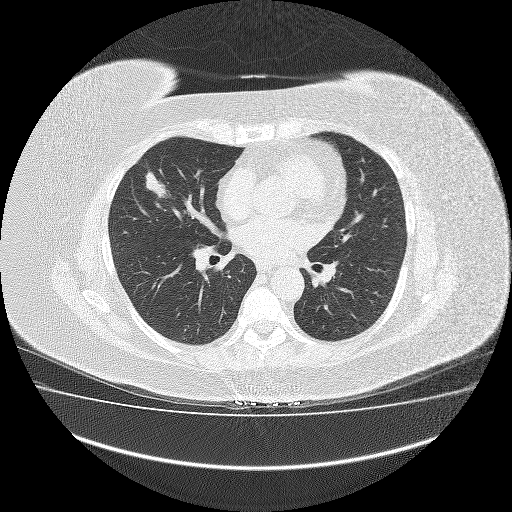
Axial slice from a low-dose chest CT screening exam. Third annual screen. Lung window (W 1500 / L -600 HU). 2 mm slice thickness. Lung (sharp) reconstruction kernel (FC51). 120 kVp. Slice 78 of 162 in the series. Female, age 64 years at enrolment. Former smoker at enrolment.
Expert reader's lesion annotation, bounding box (x1, y1, x2, y2) in pixels: (132, 167, 184, 210). Reader record for this screening exam (exam-level; its link to the box is not recorded): non-calcified nodule or mass ≥4 mm, right middle lobe, 23 × 13 mm, smooth margins, soft tissue attenuation, pre-existing on the prior screen: no. Lung cancer was diagnosed 31 days after this screen: carcinoid tumor, NOS, right middle lobe, 3 mm at pathology.